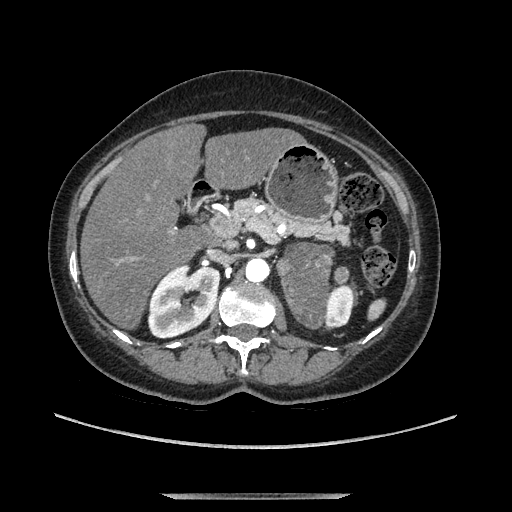
Contrast-enhanced abdominal CT, one axial slice; slice 67 of 169 in the series (ordered by position); soft-tissue window (W 400 / L 40 HU); 1.25 mm slice thickness; 512 × 512 image matrix. Female patient. Case-level facts recorded for this patient, not image findings: diagnosis: adrenocortical carcinoma; tumour side: left adrenal; tumour size at pathology: 9 cm.
Annotated regions visible in this slice (semi-automatic segmentation, software-assisted and operator-edited):
- mass: bounding box (x1, y1, x2, y2) in pixels: (279, 245, 329, 325)